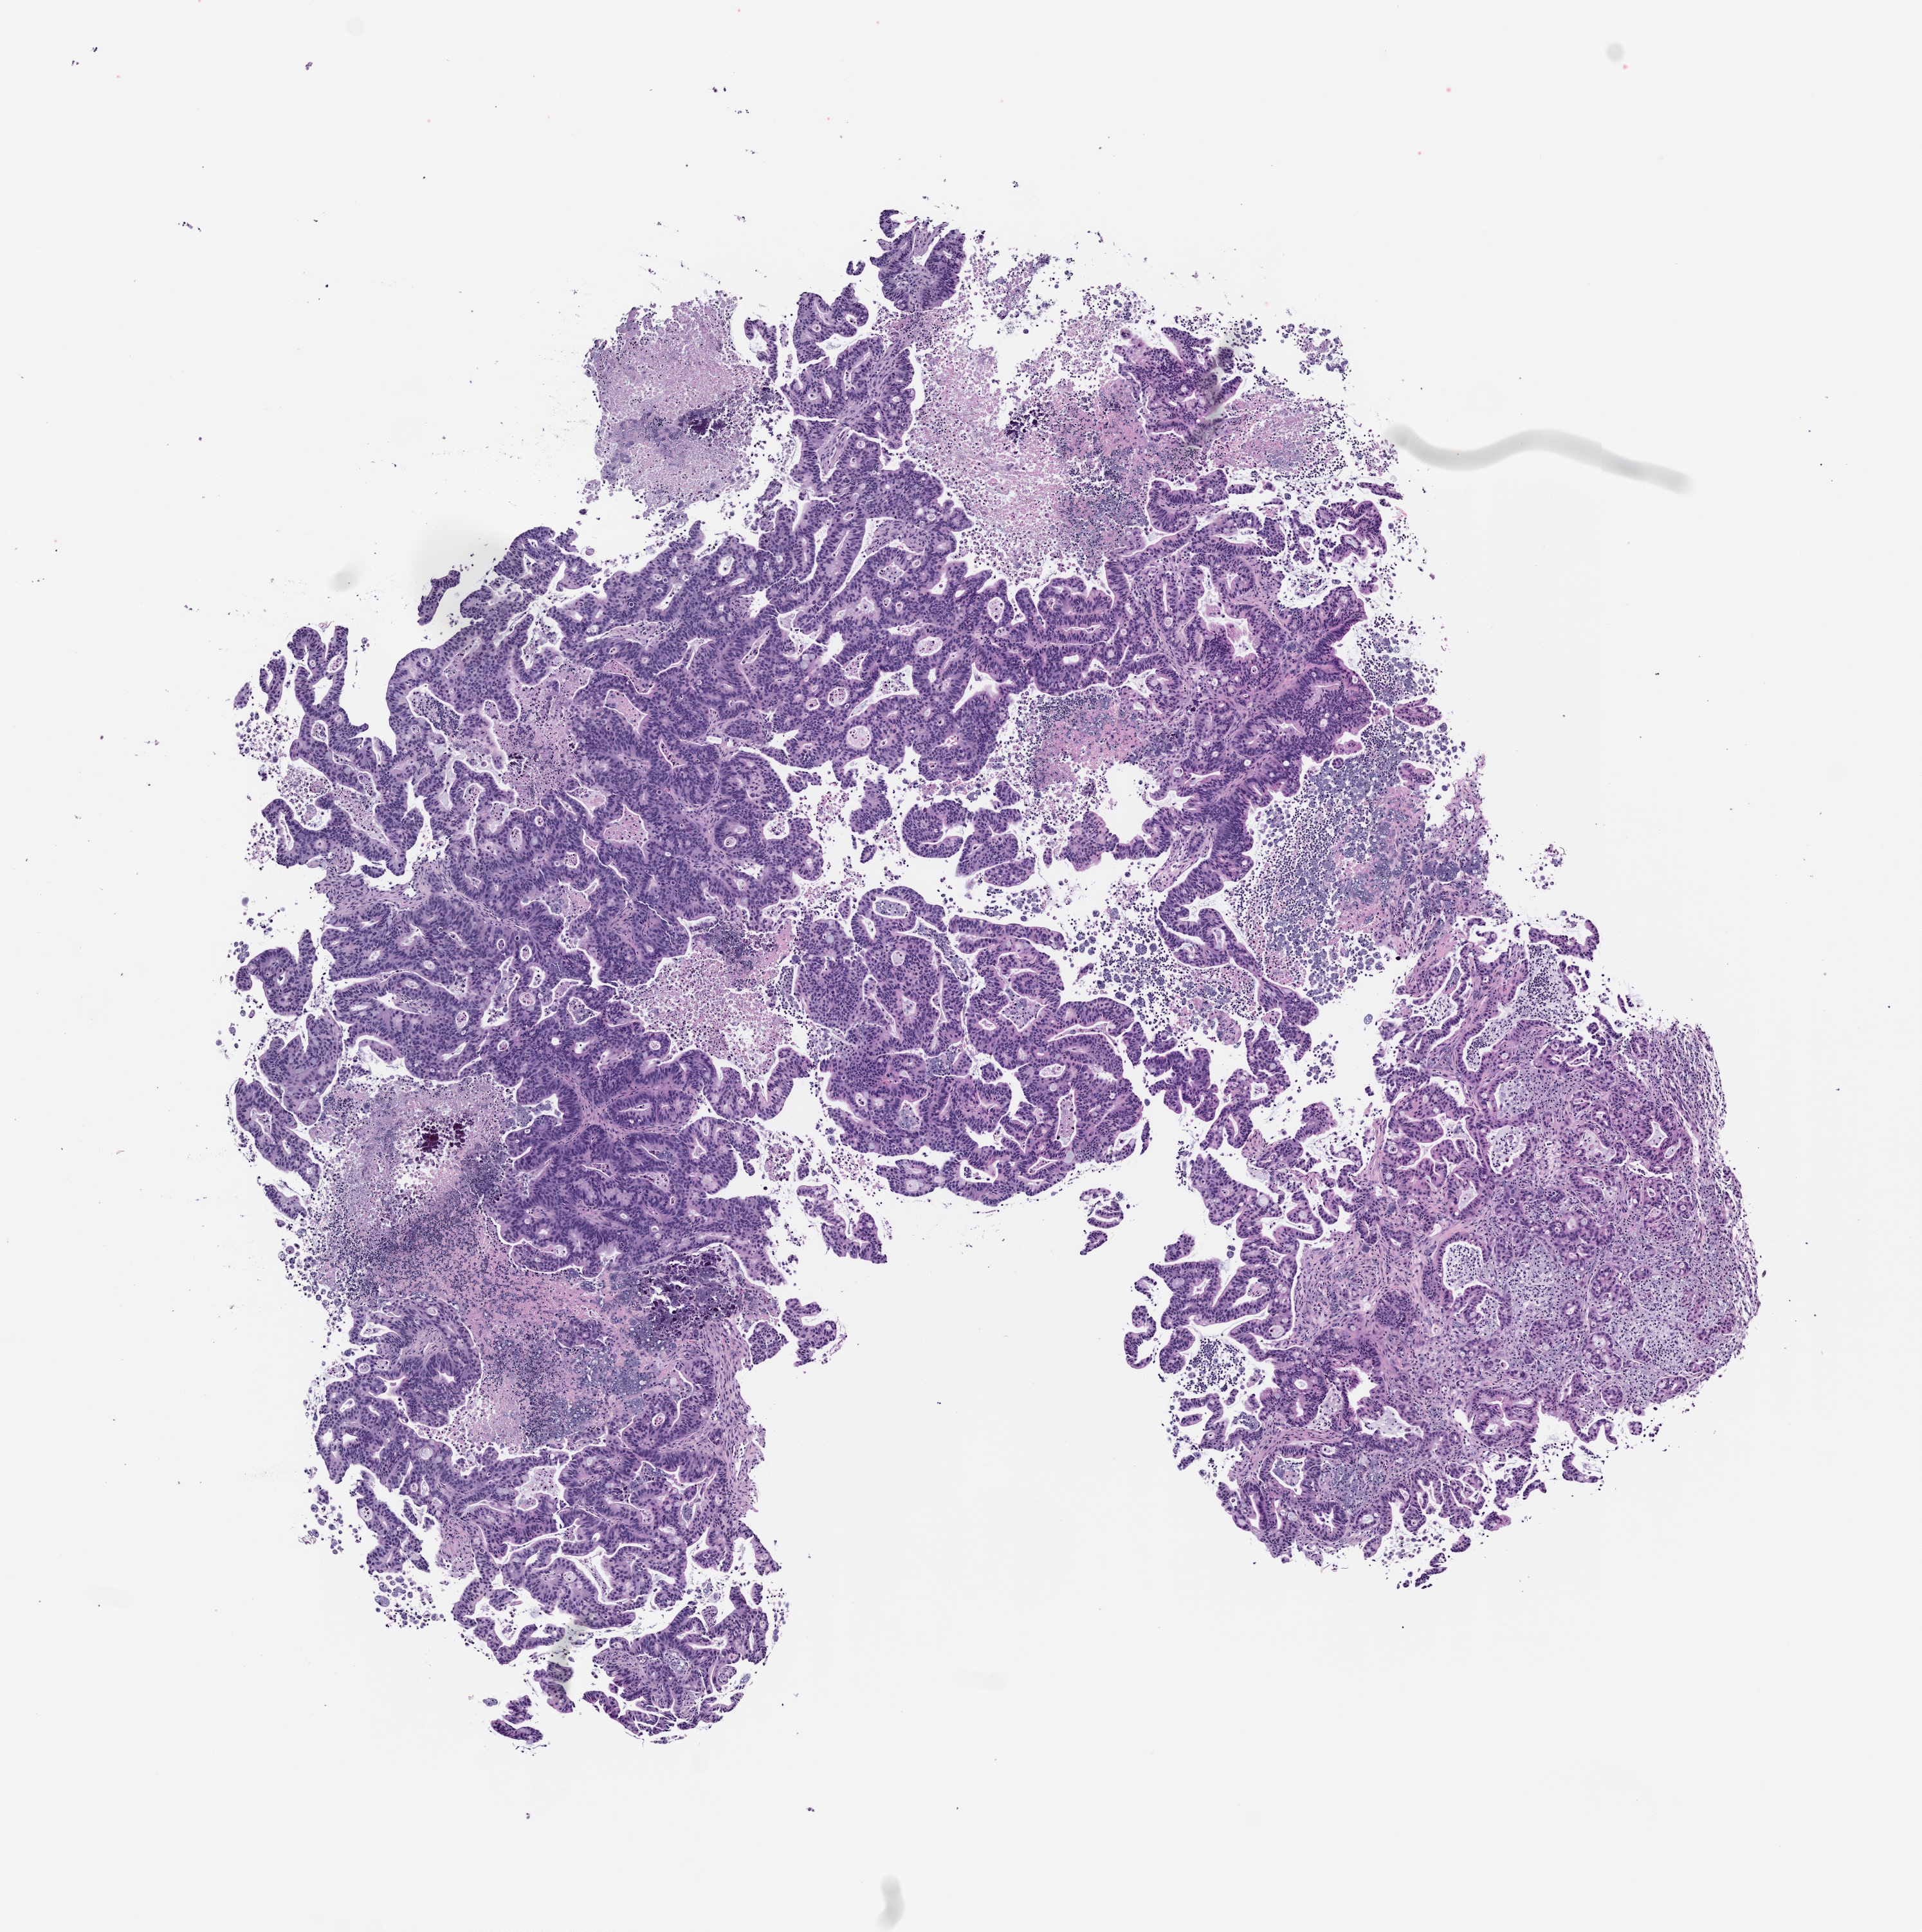
Whole-slide image, haematoxylin and eosin: patient-derived xenograft (human tumor grown in a mouse), whole scanned area (about 6.0 x 6.0 mm) shown as a low-resolution overview, formalin-fixed paraffin-embedded section, tumor site category: small intestine.
Originating patient diagnosis: Small Intestinal Adenocarcinoma.